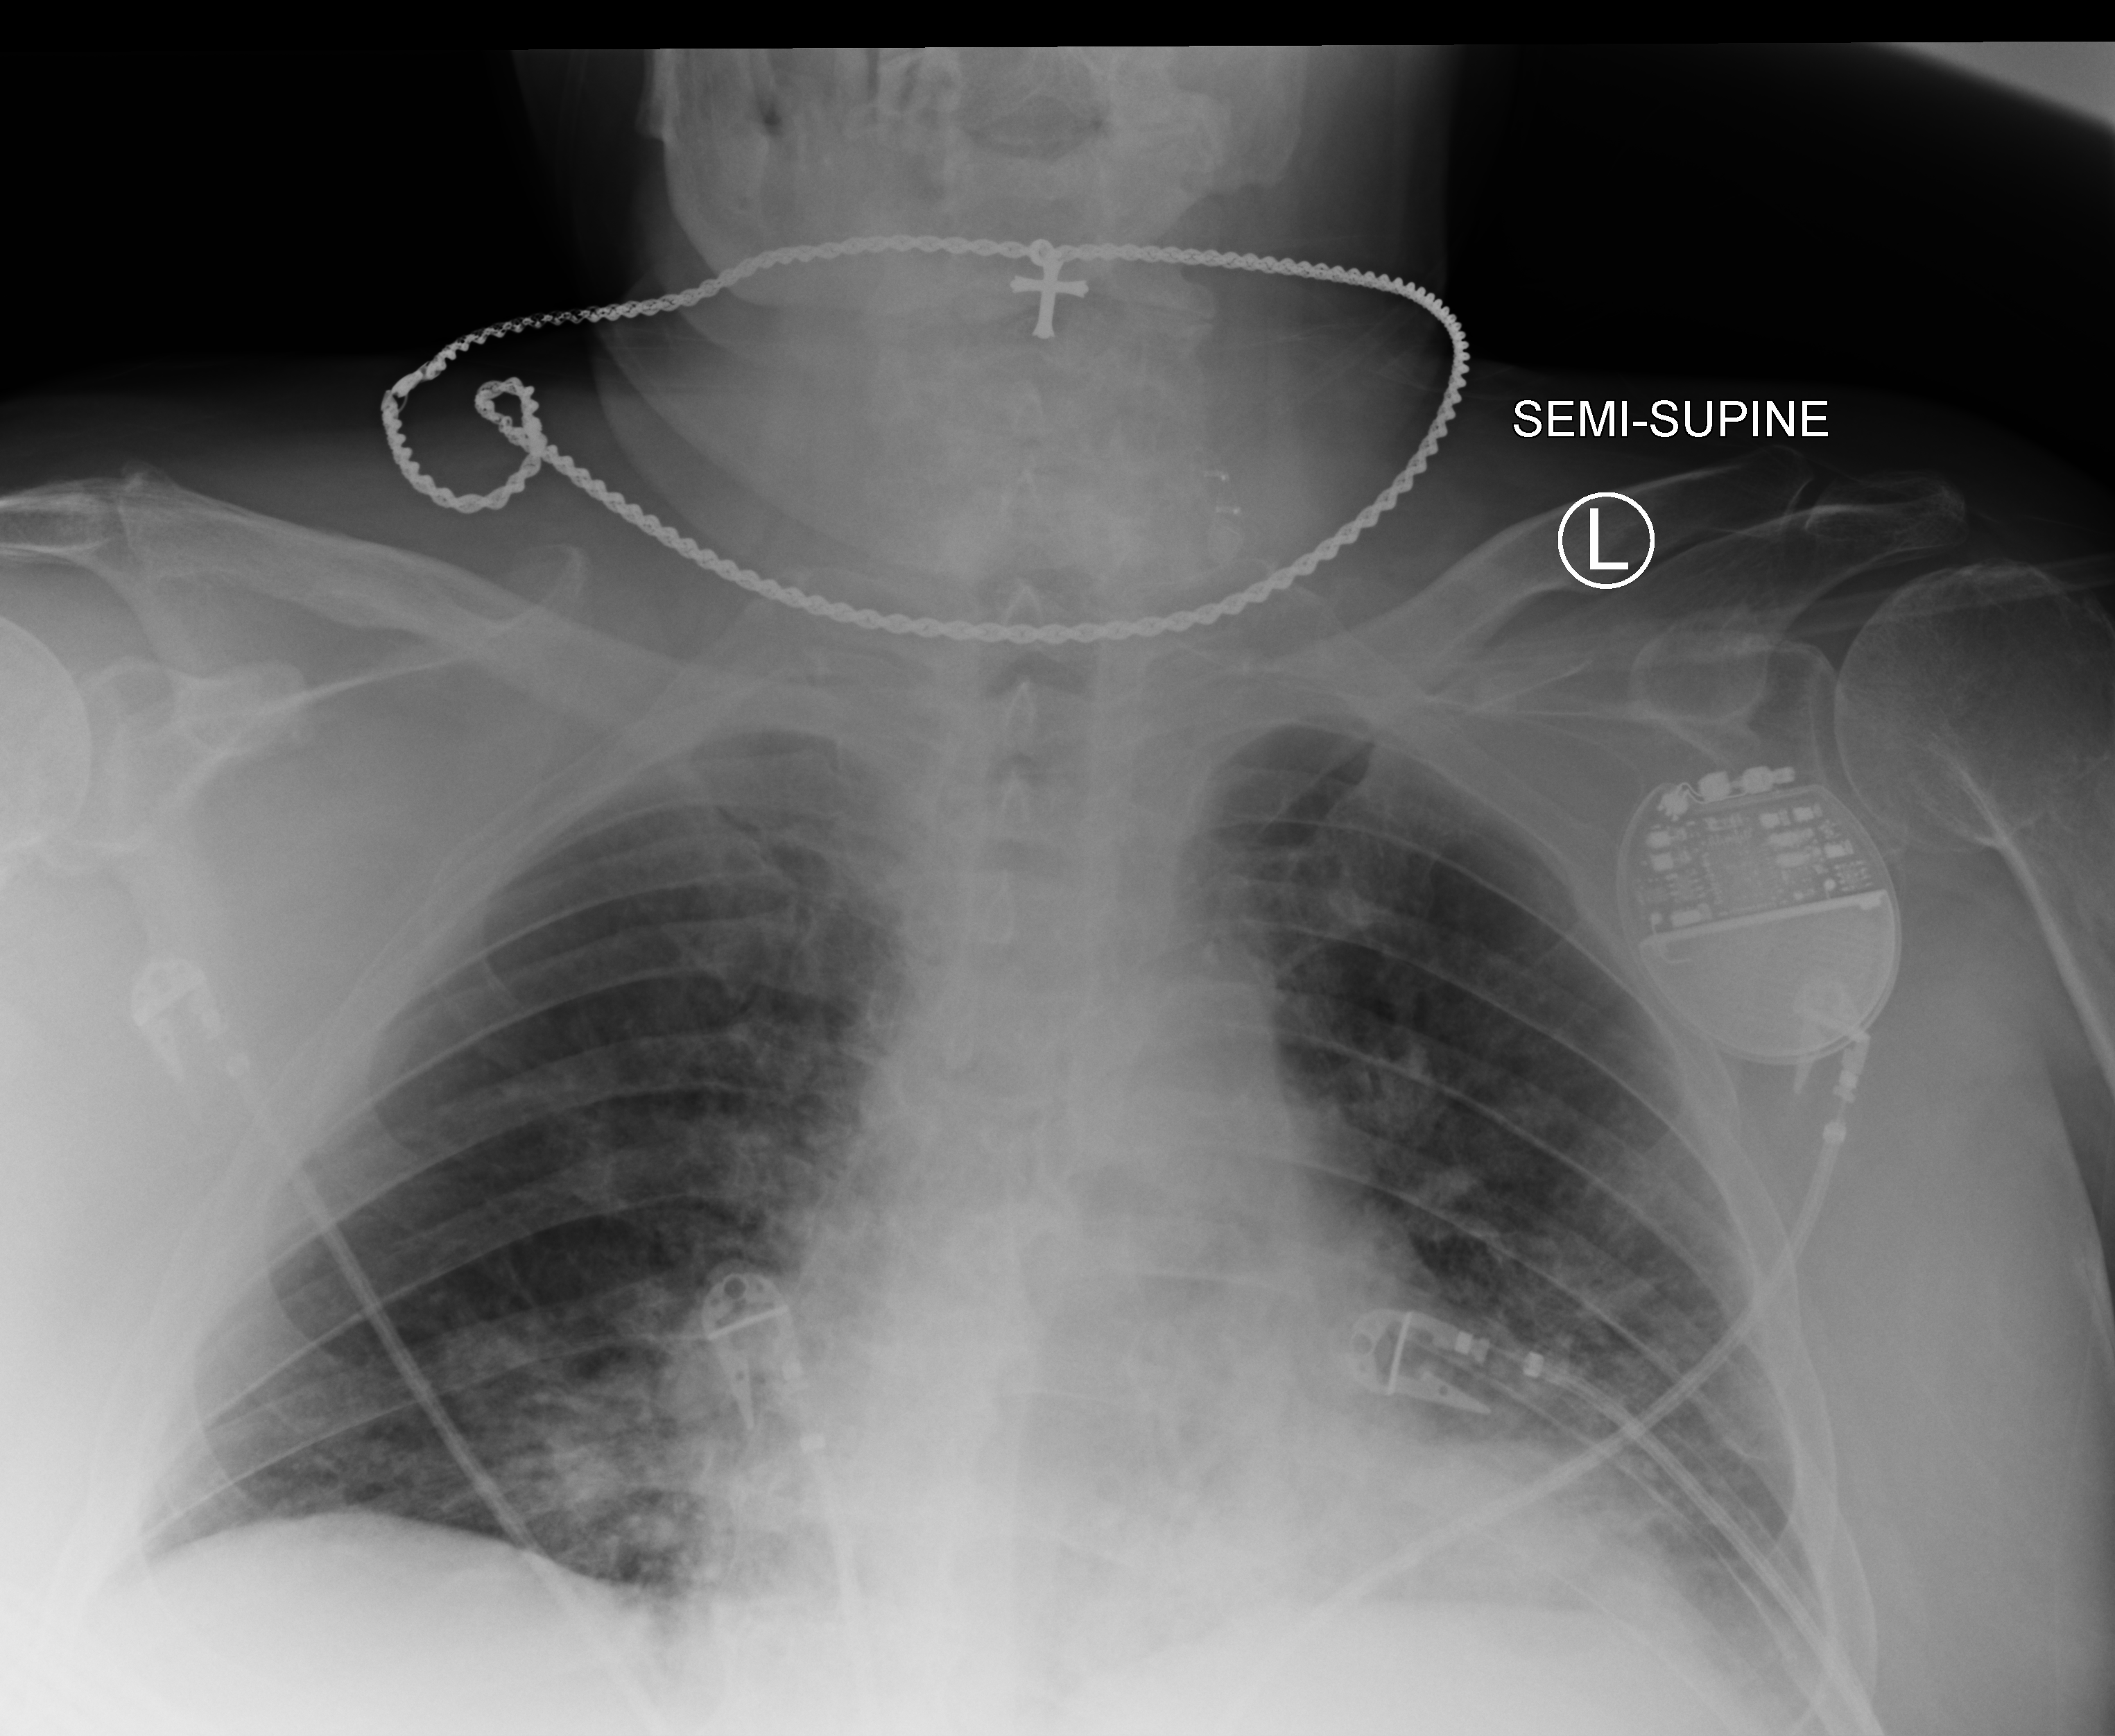
Chest X-ray (portable), anteroposterior (AP) projection. Male patient hospitalised with COVID-19, age 60–74 years.
Hospital-stay facts (about this admission, not read from this image; timing relative to this image not recorded): length of hospital stay: 23 days.